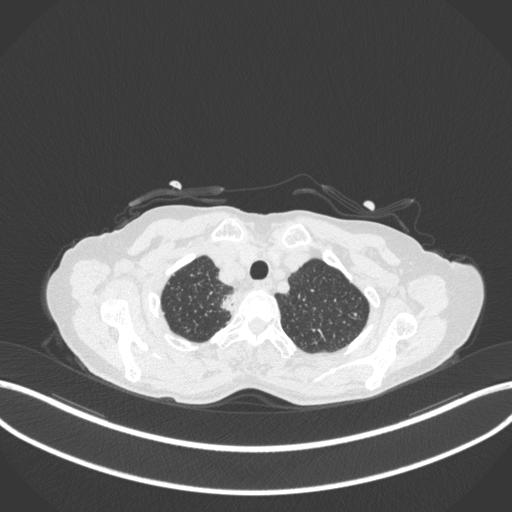
Chest CT, one axial slice. Slice 331 of 363 in the series (ordered by position). Reconstruction kernel B31f. 120 kVp. Lung window (W 1500 / L -600 HU). 512 × 512 image matrix. Female patient, age 75 years. From the clinical record (not read from this slice): clinical TNM (as recorded): T1c N1 M1.
Outlined on this slice (bounding box drawn by a radiologist):
- lung tumour (recorded histology: adenocarcinoma): bounding box [x1, y1, x2, y2] px = [216, 291, 241, 313]